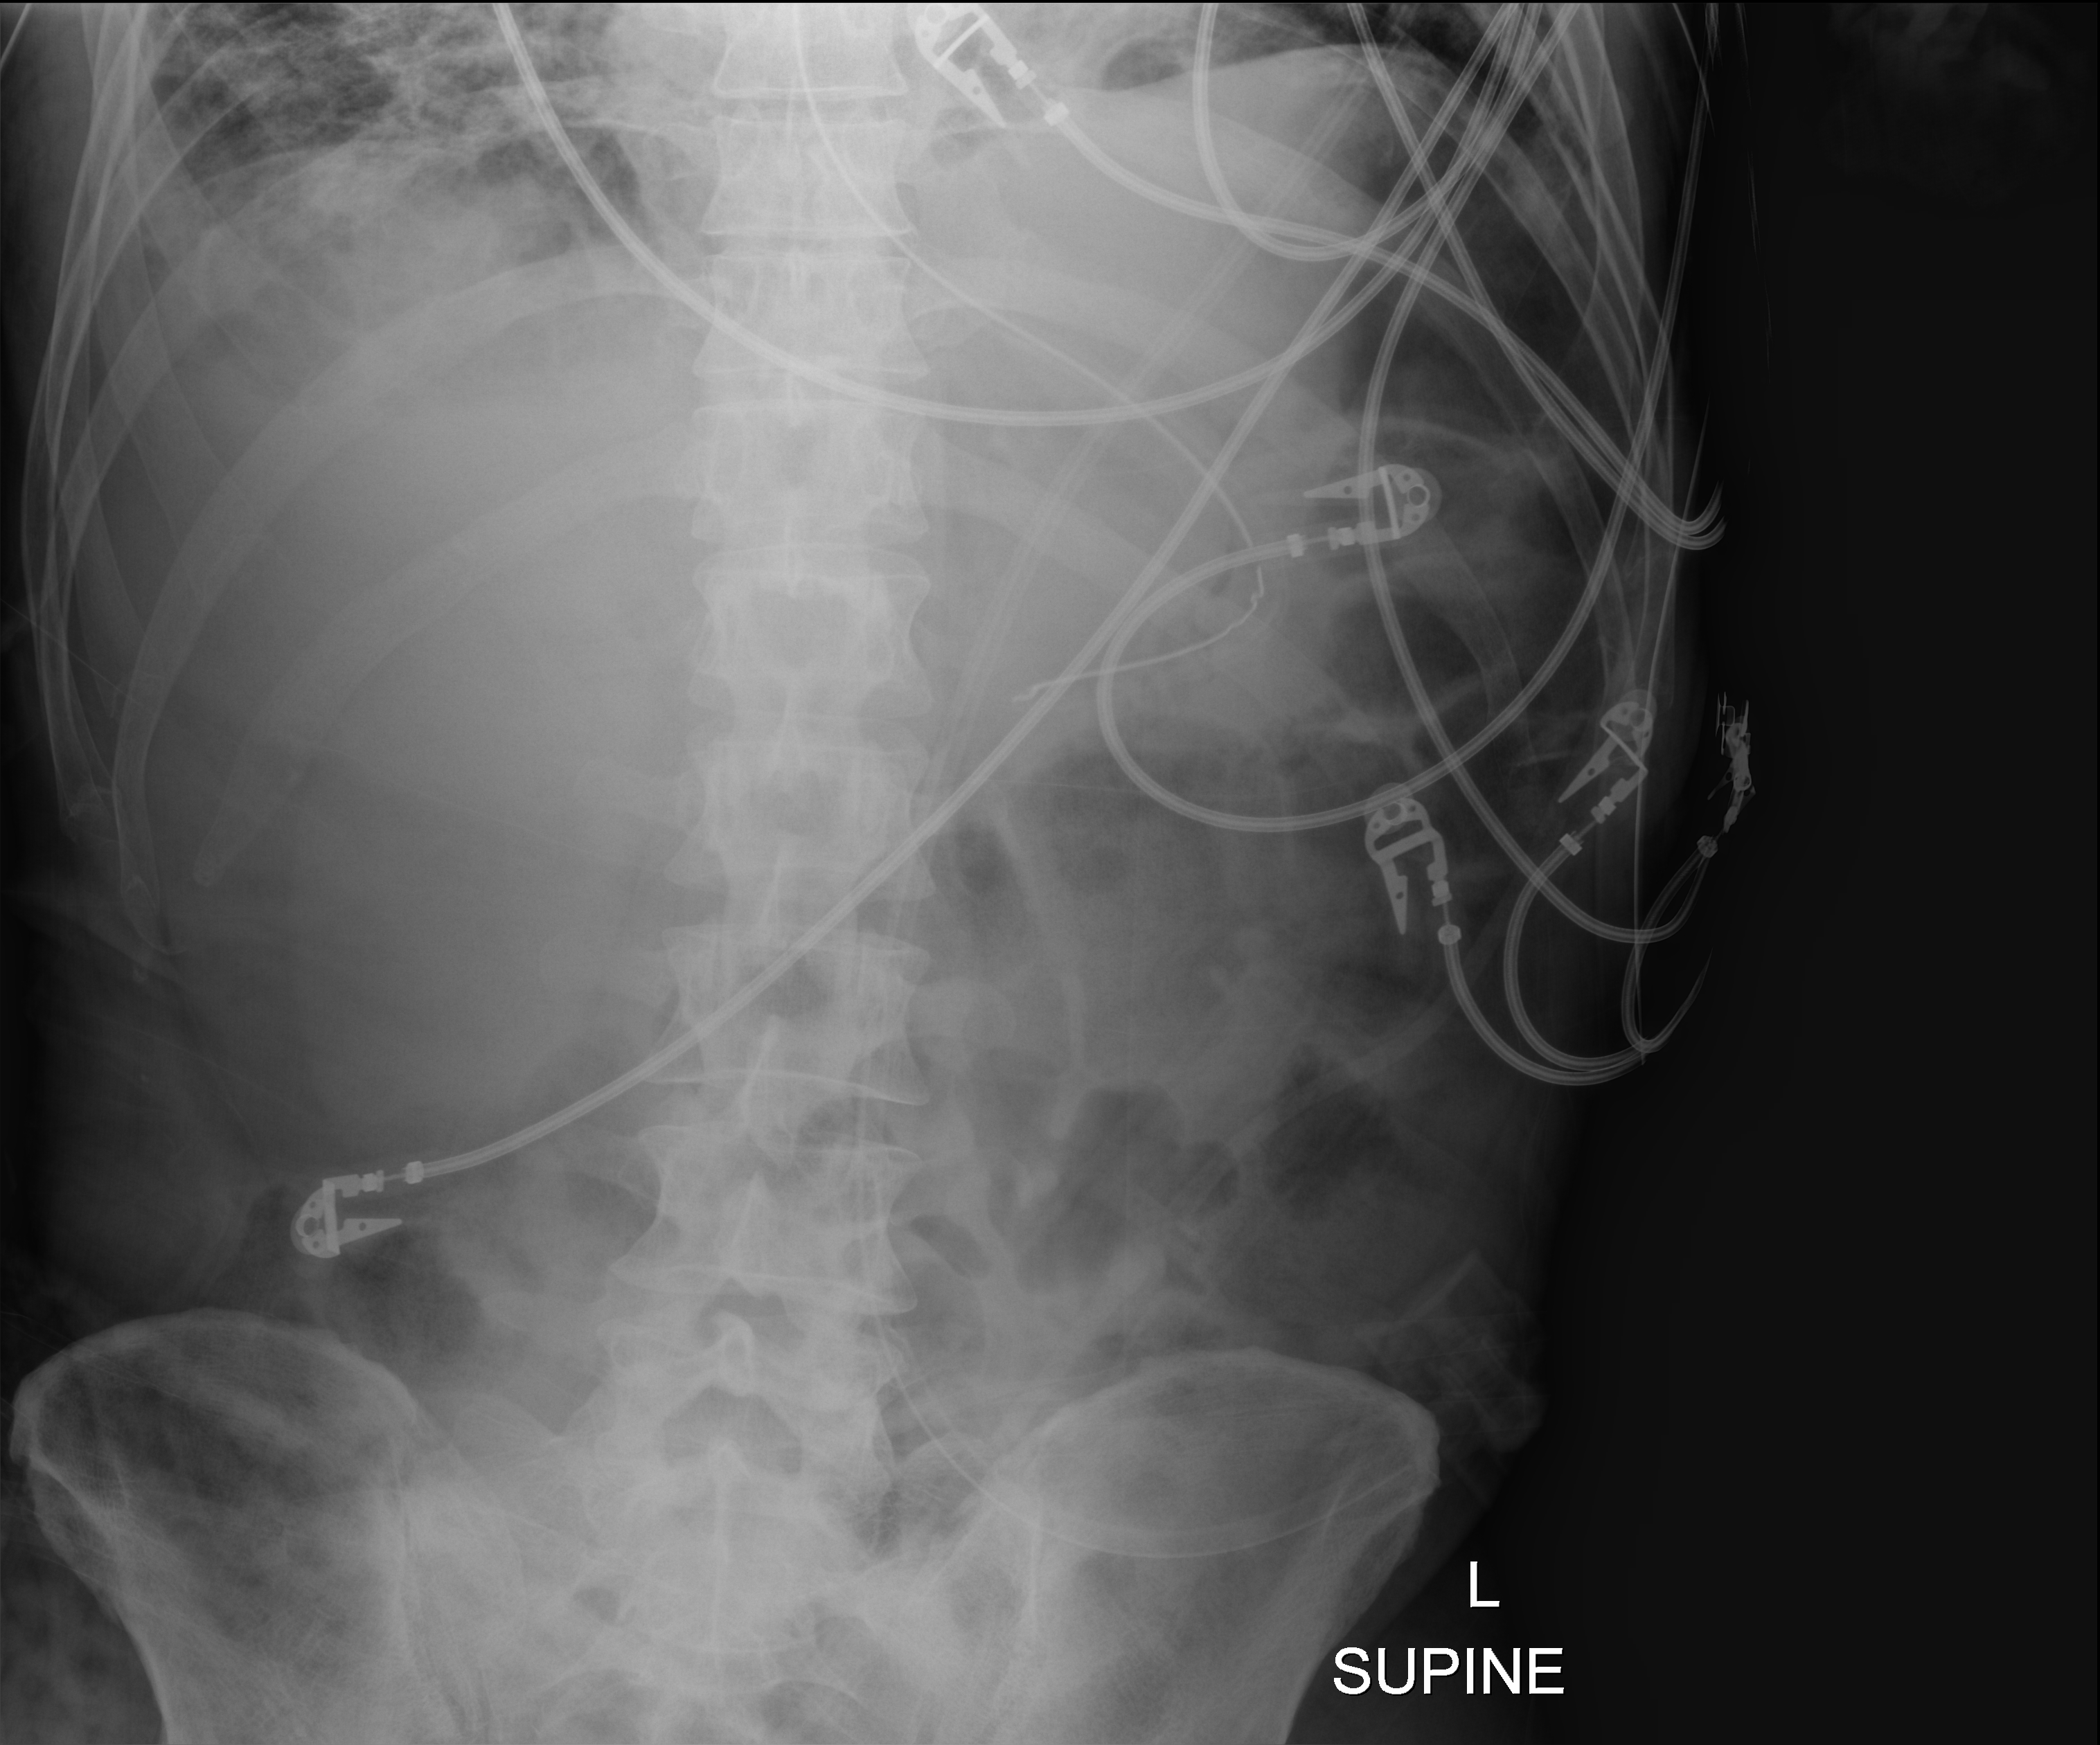
Bedside abdomen radiograph (digital radiography), anteroposterior (AP) projection. Male patient hospitalised with COVID-19, age 18–59 years.
Admission-level facts for this patient (not findings on this image; timing relative to this image not recorded):
- COPD (admission record): no